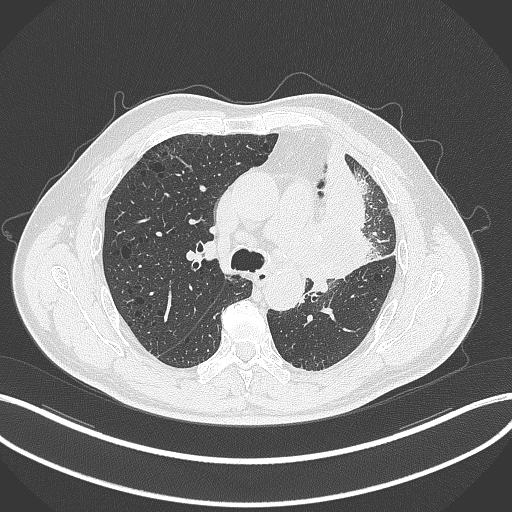
Chest CT, one axial slice. Slice 197 of 297 in the series (ordered by position). Reconstruction kernel B70f. 120 kVp. Lung window (W 1500 / L -600 HU). 512 × 512 image matrix, field of view 400 × 400 mm. Male patient, age 68 years. Case-level facts recorded for this patient, not image findings: clinical TNM (as recorded): T3 N3 M1.
Annotated regions visible in this slice (bounding box drawn by a radiologist):
- lung tumour (recorded histology: adenocarcinoma): bounding box (x1, y1, x2, y2) in pixels: (304, 157, 383, 286)